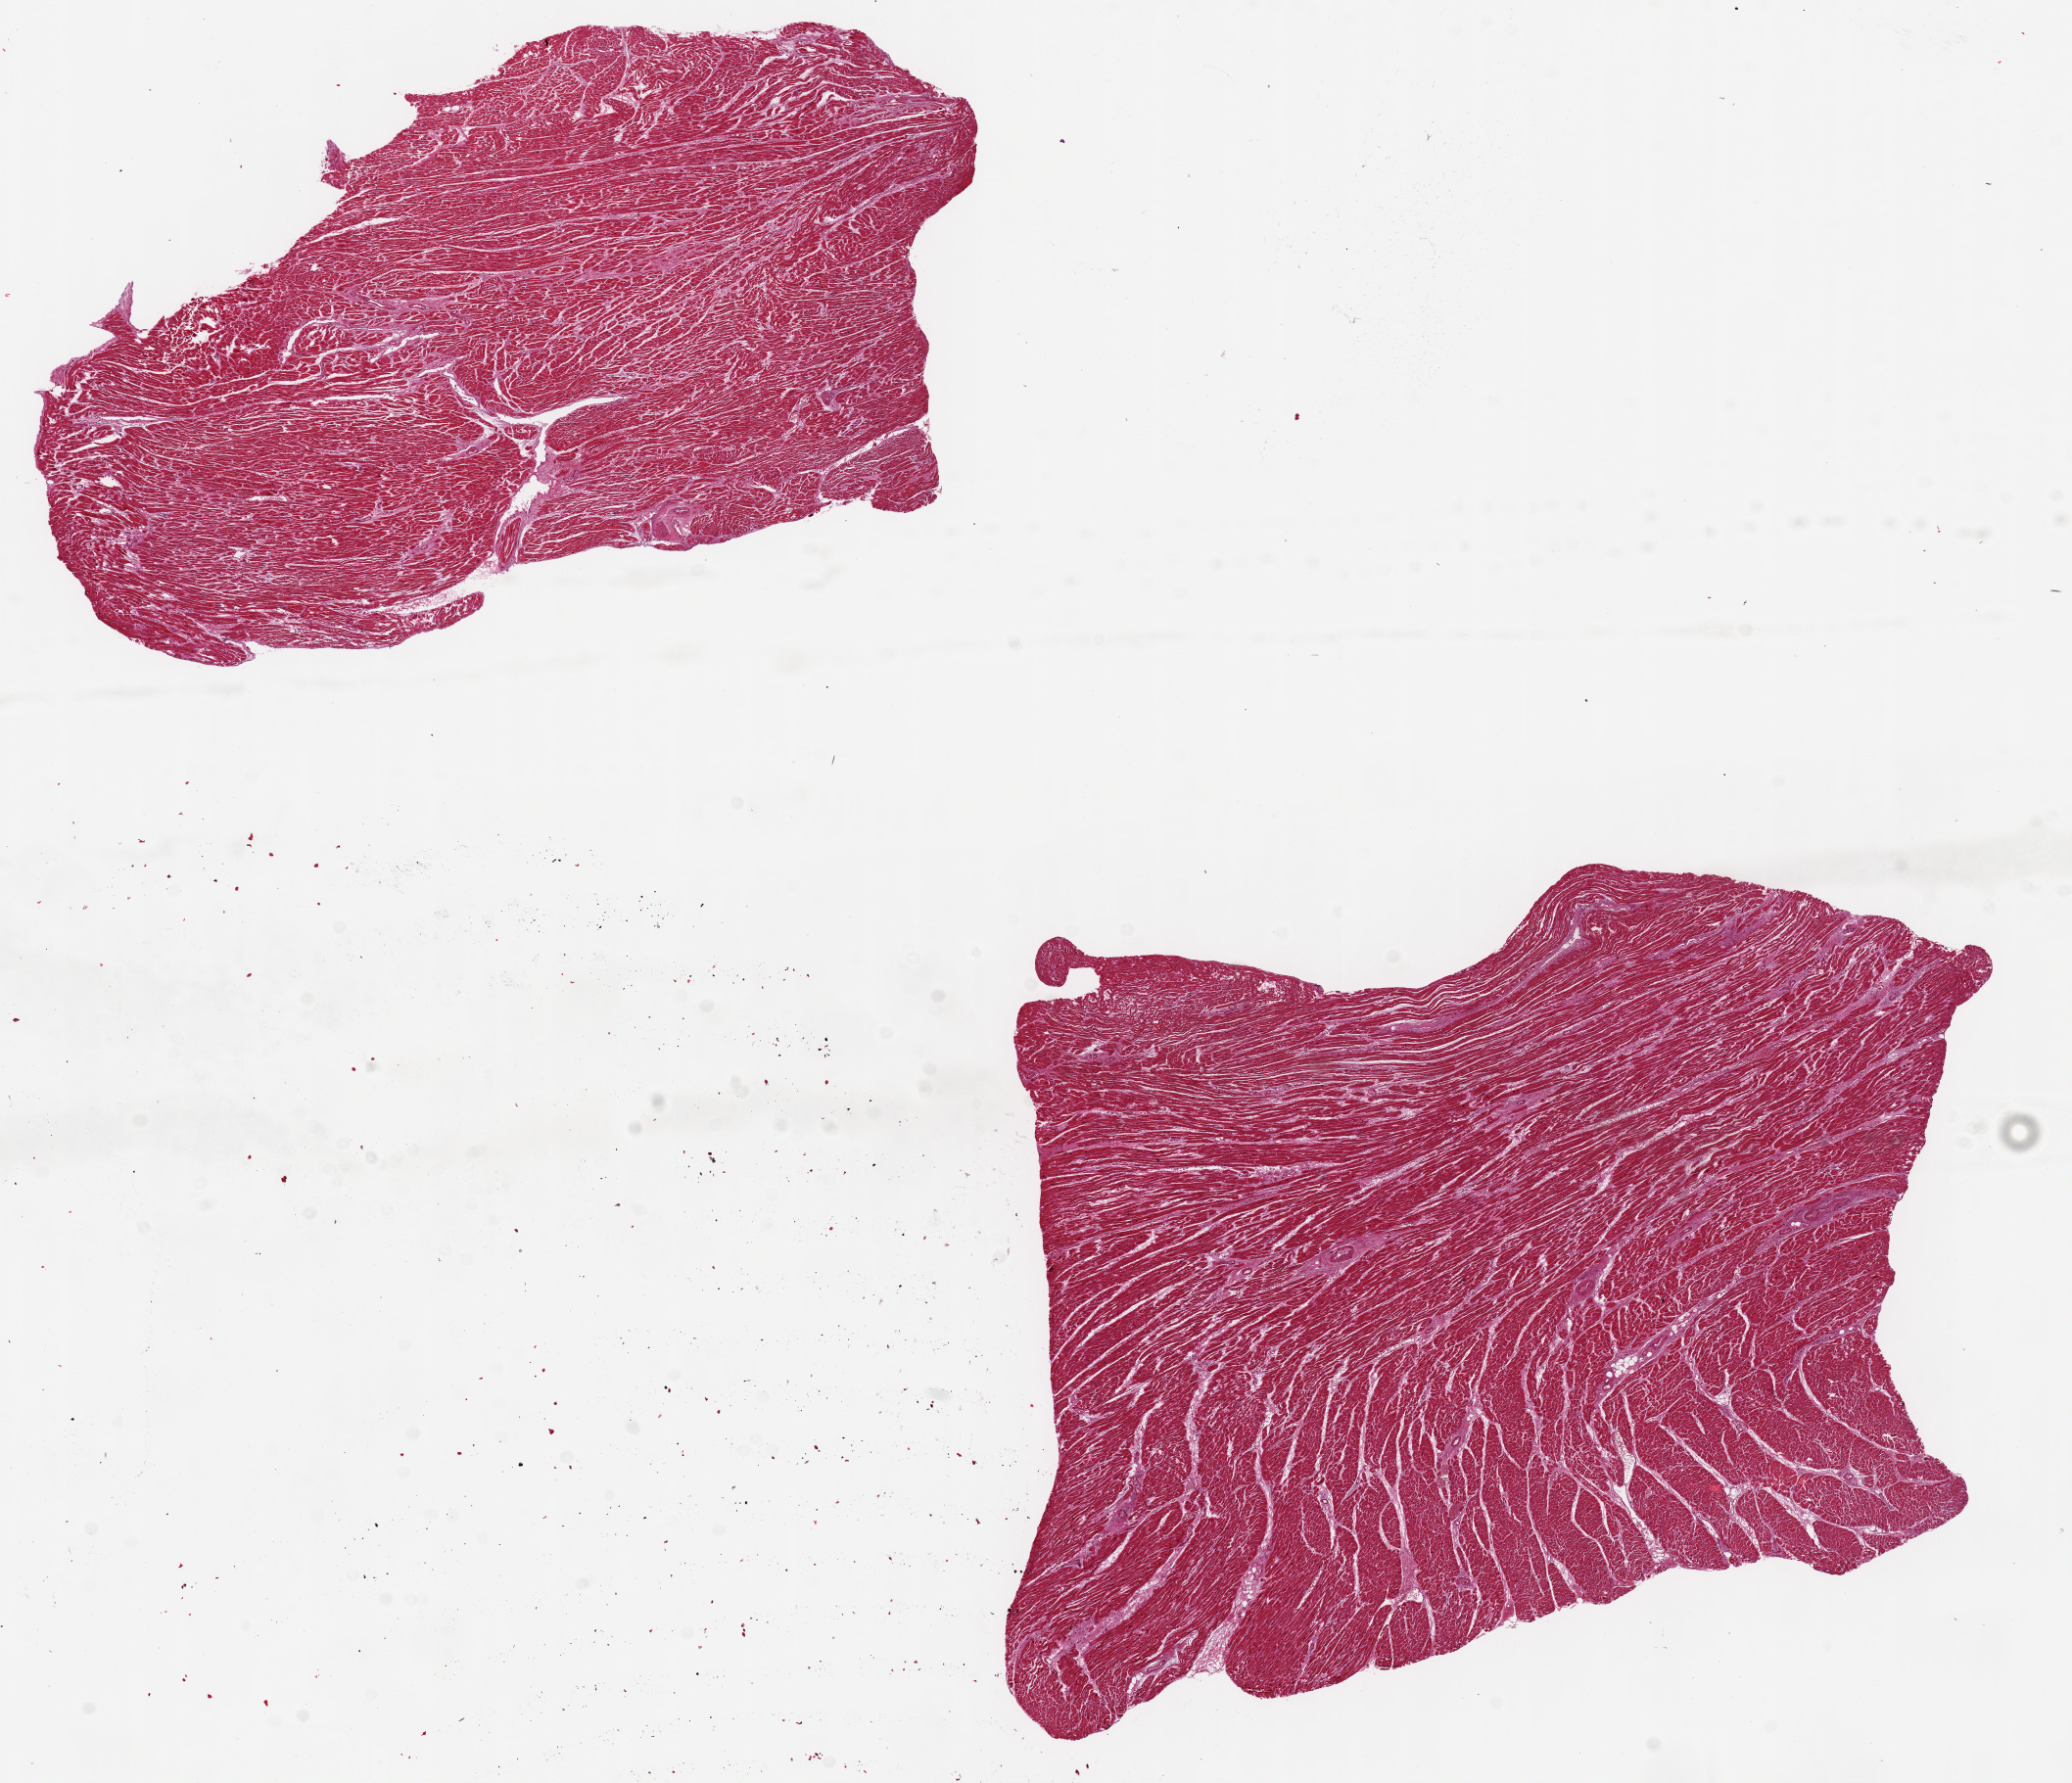
H&E whole-slide image, brightfield — shown as a low-resolution overview of the whole scanned area (about 16.7 x 14.4 mm), PAXgene-fixed, paraffin-embedded tissue, target tissue: heart, donor tissue sample. Donor sex: male.
Review note (as recorded): 2 pieces ~7x4mm.